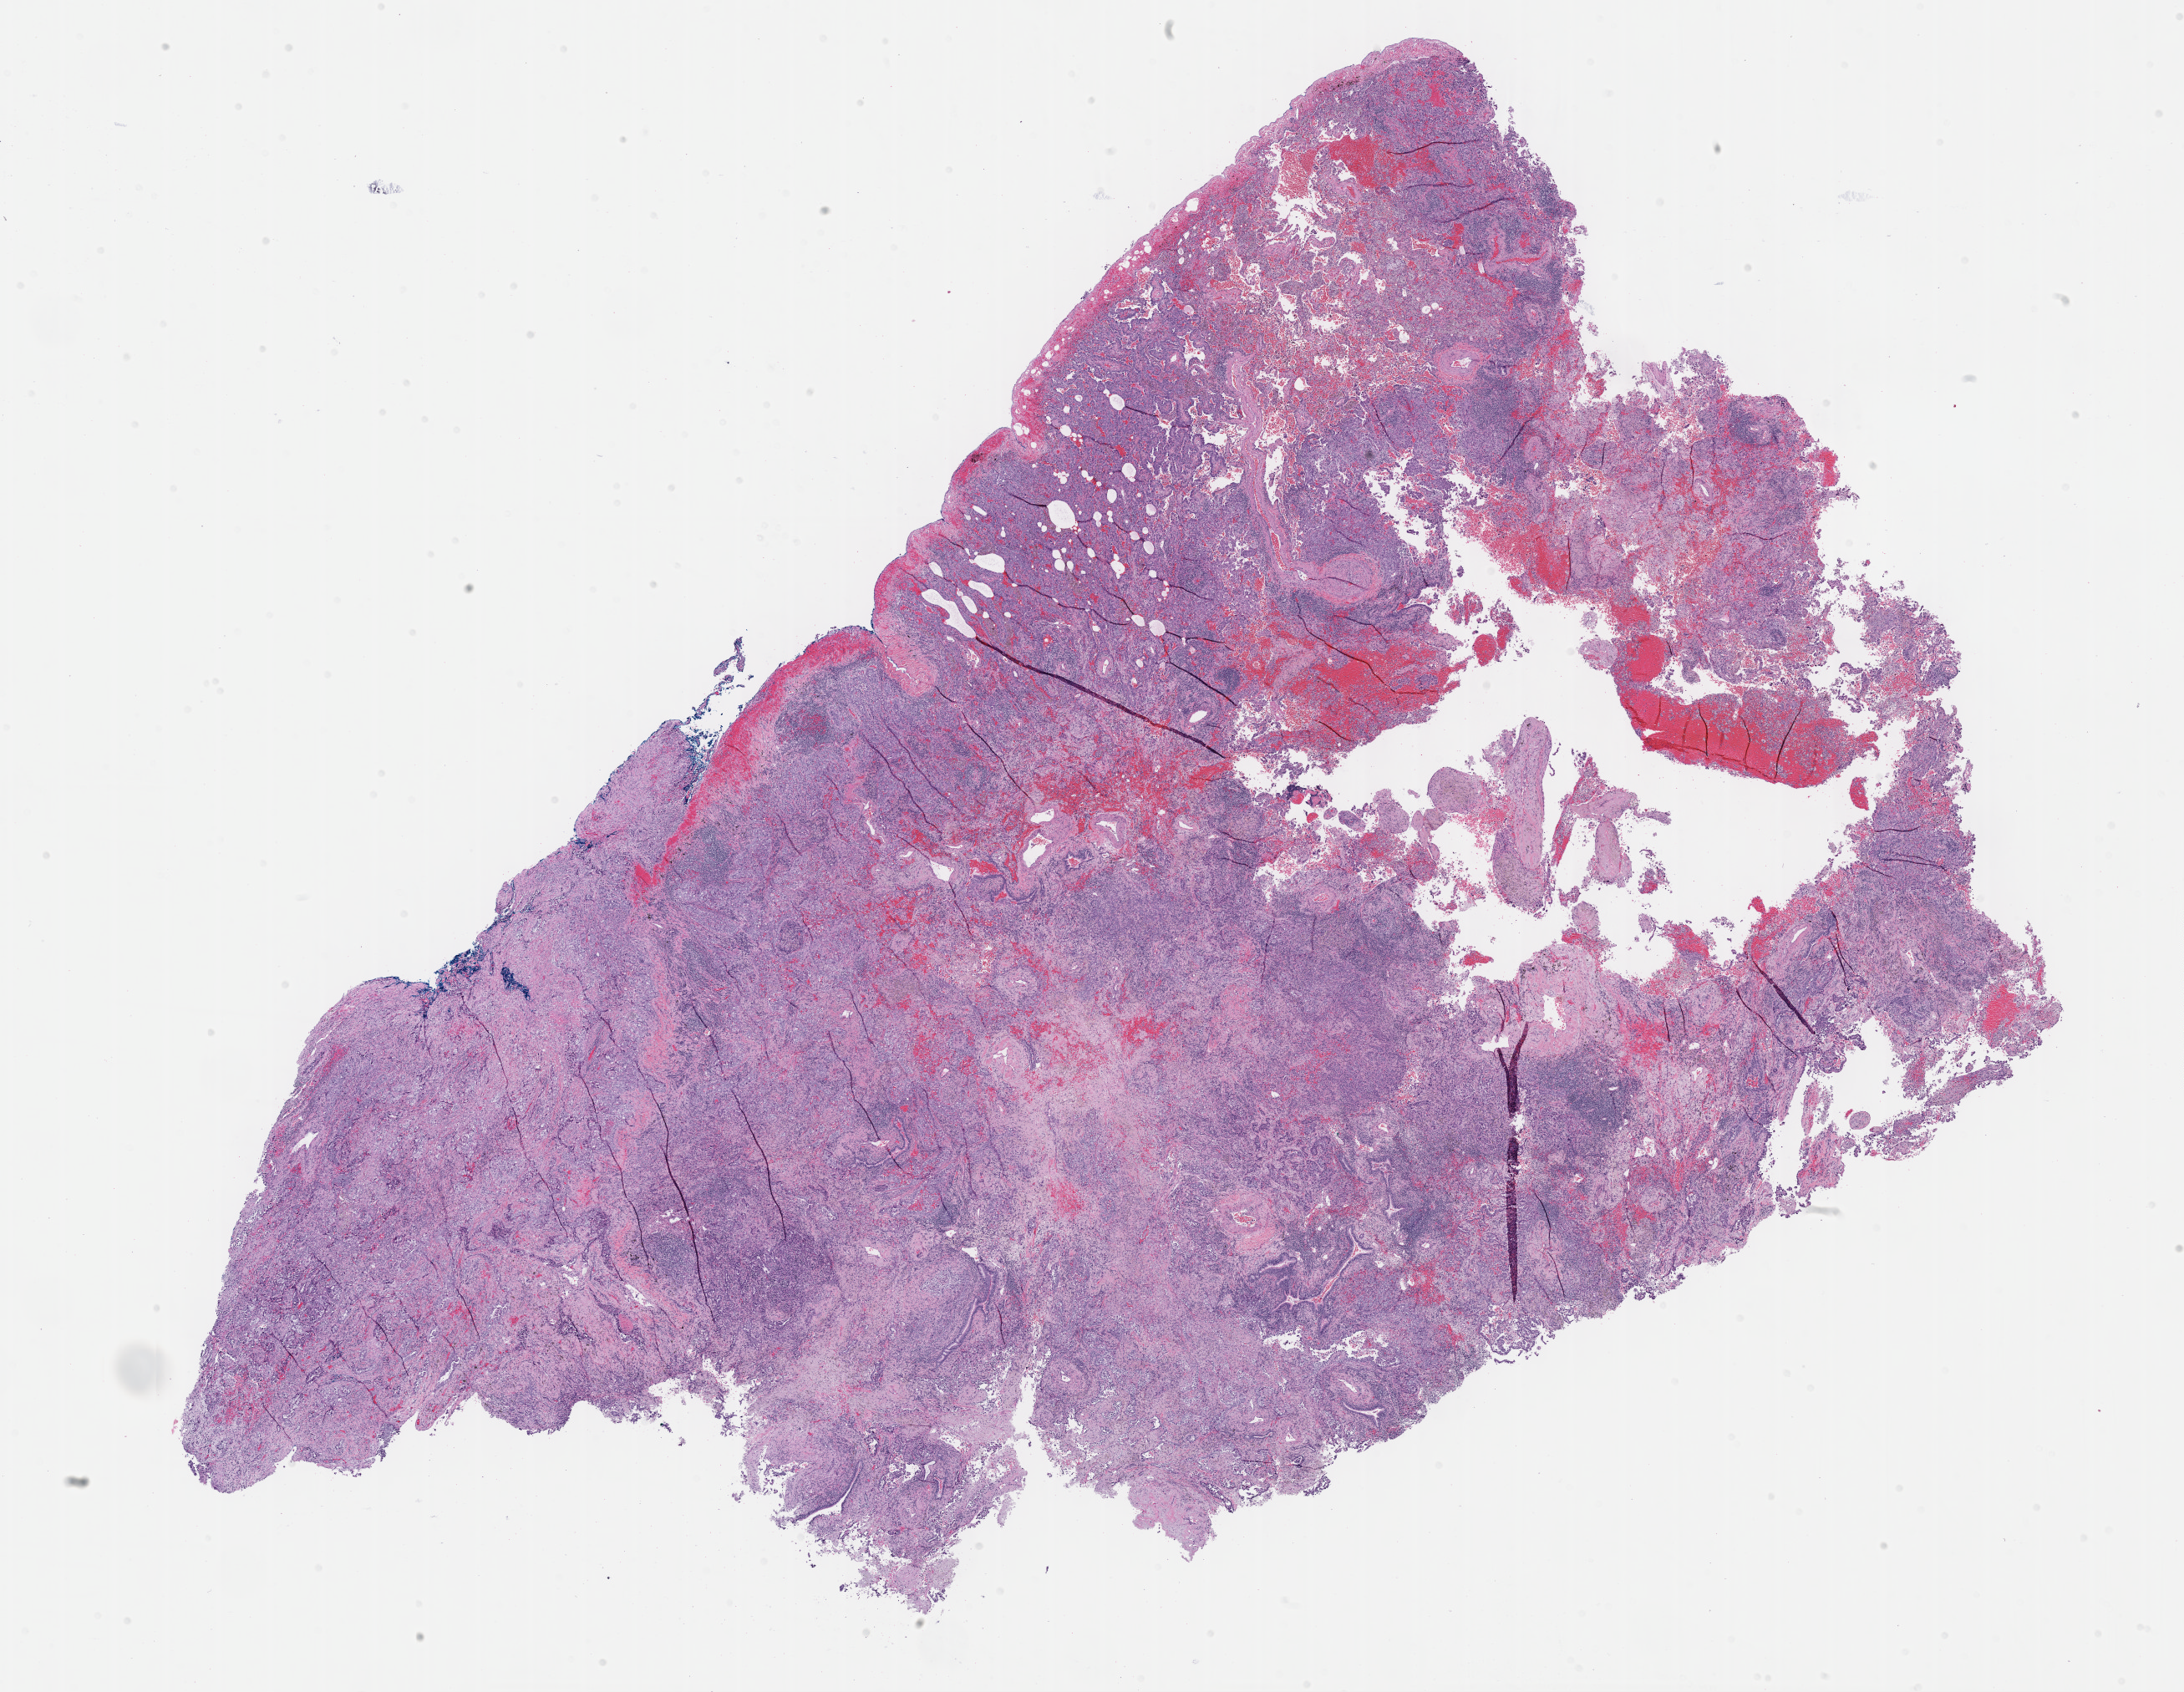
Digitized Hematoxylin and eosin (H&E) stained tissue section (whole slide), shown as a low-resolution overview of the whole scanned area (about 21.1 x 16.4 mm, acquisition: 40x scan); formalin-fixed paraffin-embedded (FFPE) diagnostic section; sample: primary tumour, lung. Male, age 56 years at initial diagnosis.
Diagnosis: Adenocarcinoma, NOS. AJCC pathologic stage: IIA.